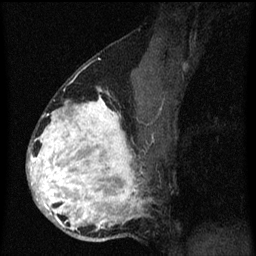
Breast MRI (dynamic contrast-enhanced), one sagittal slice. Position 37 of 60 along the scan axis. Dynamic contrast-enhanced series, image 2 of 3 at this slice position (ordered by acquisition). 1.5 T. TE 4.2 ms, TR 8.4 ms. 2 mm slice thickness. 256 × 256 image matrix, field of view 180 × 180 mm. Patient: female, 34 years. Case-level facts recorded for this patient, not image findings: setting: breast cancer imaged before/during neoadjuvant chemotherapy; receptor status: HR-positive, HER2-negative.
Annotated regions visible in this slice (semi-automatically segmented with operator editing):
- analysis volume of interest (the breast-tissue region the enhancement analysis was run in; not a lesion): bounding box <28,58,159,243> (left, top, right, bottom; pixels)
- tumour enhancement mask (voxels above the 70 % enhancement threshold inside the analysis volume of interest): <28,90,149,231>